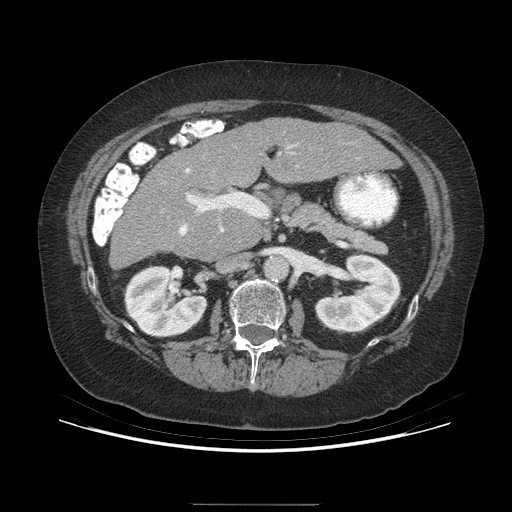
Contrast-enhanced abdominal CT (liver protocol), one axial slice. 140 kVp. Soft-tissue window (W 400 / L 40 HU). 512 × 512 image matrix, field of view 400 × 400 mm. Case-level facts recorded for this patient, not image findings: diagnosis: hepatocellular carcinoma (patient treated with transarterial chemoembolisation; whether this scan precedes or follows treatment is not stated here); TNM stage (as recorded): Stage-I; Child-Pugh class: A.
Annotated regions visible in this slice (semi-automatically segmented with operator editing):
- liver parenchyma outside the tumour (the mass and vessels are separate outlines, so this box may not span the whole liver): bounding box [x1, y1, x2, y2] px = [110, 118, 400, 268]
- liver vessels: [179, 146, 292, 235]